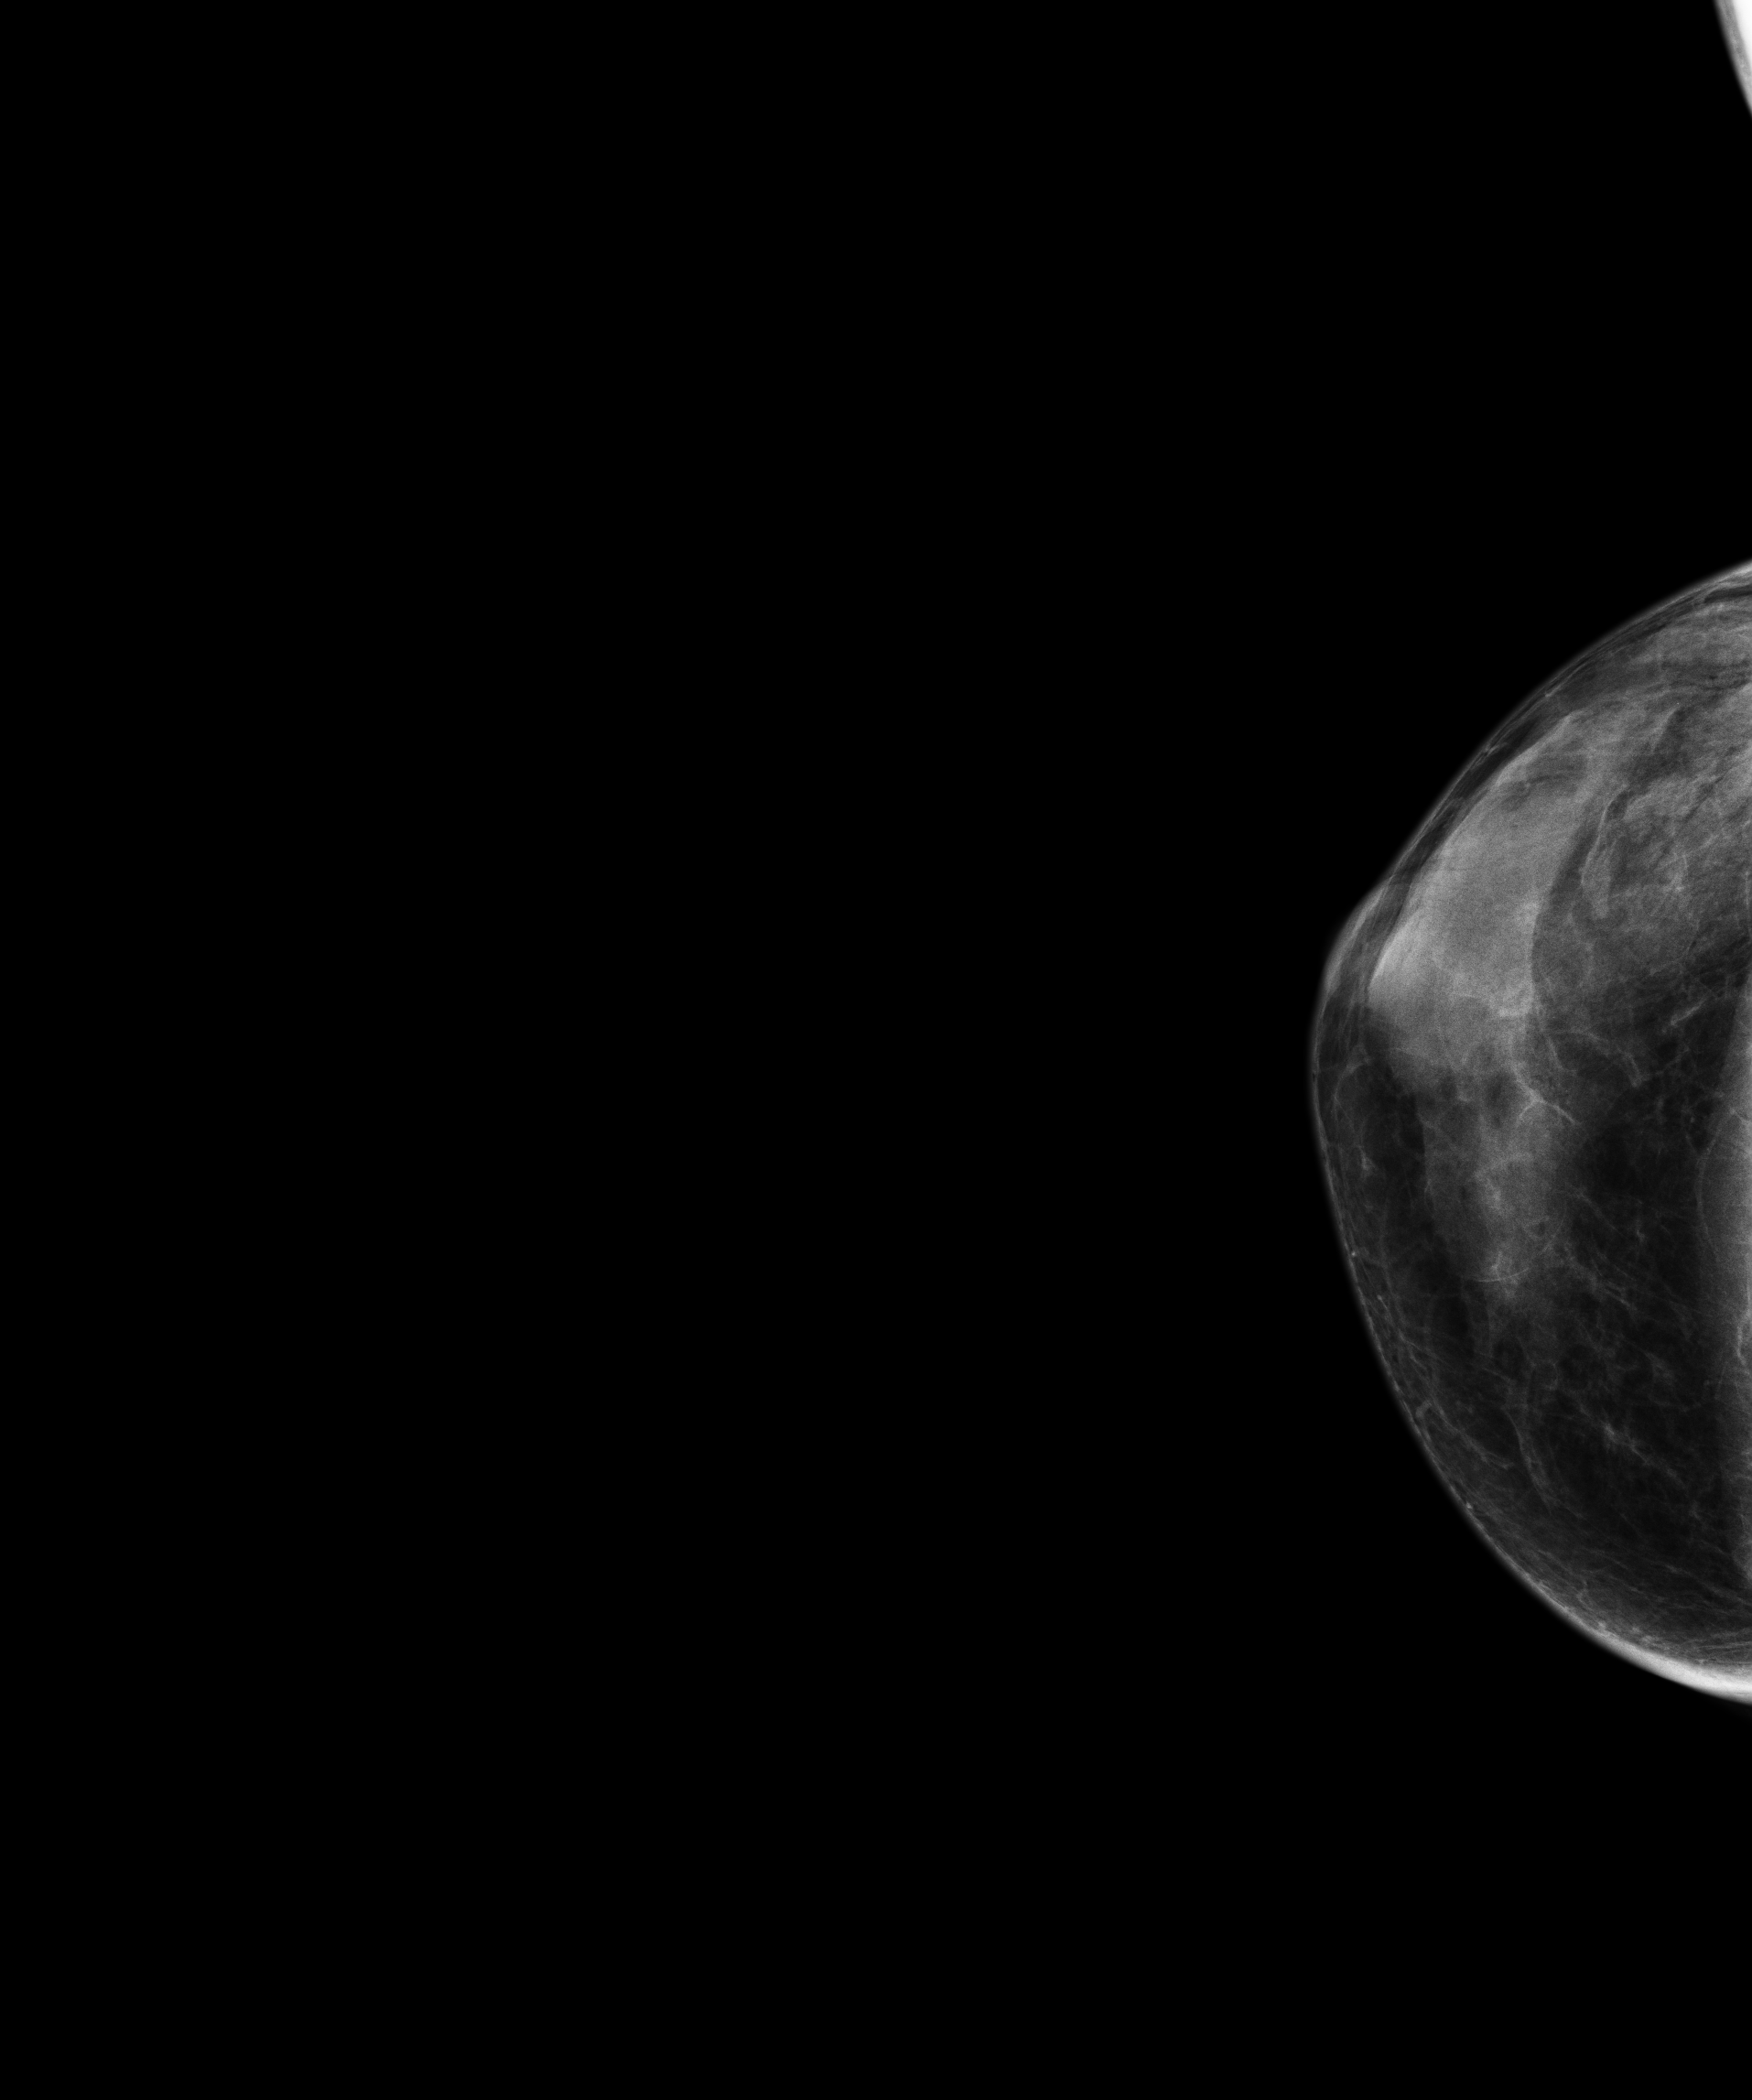
Full-field digital mammogram (FFDM), right breast, cranio-caudal projection, screening examination, compressed breast thickness 27 mm. Female patient, age 55 years.
- BI-RADS breast density category at the screening exam (both breasts, scale 1–4): 4
- final BI-RADS category for the screening round (tomosynthesis exam, both breasts): category 1
- recall: no recall after this screen